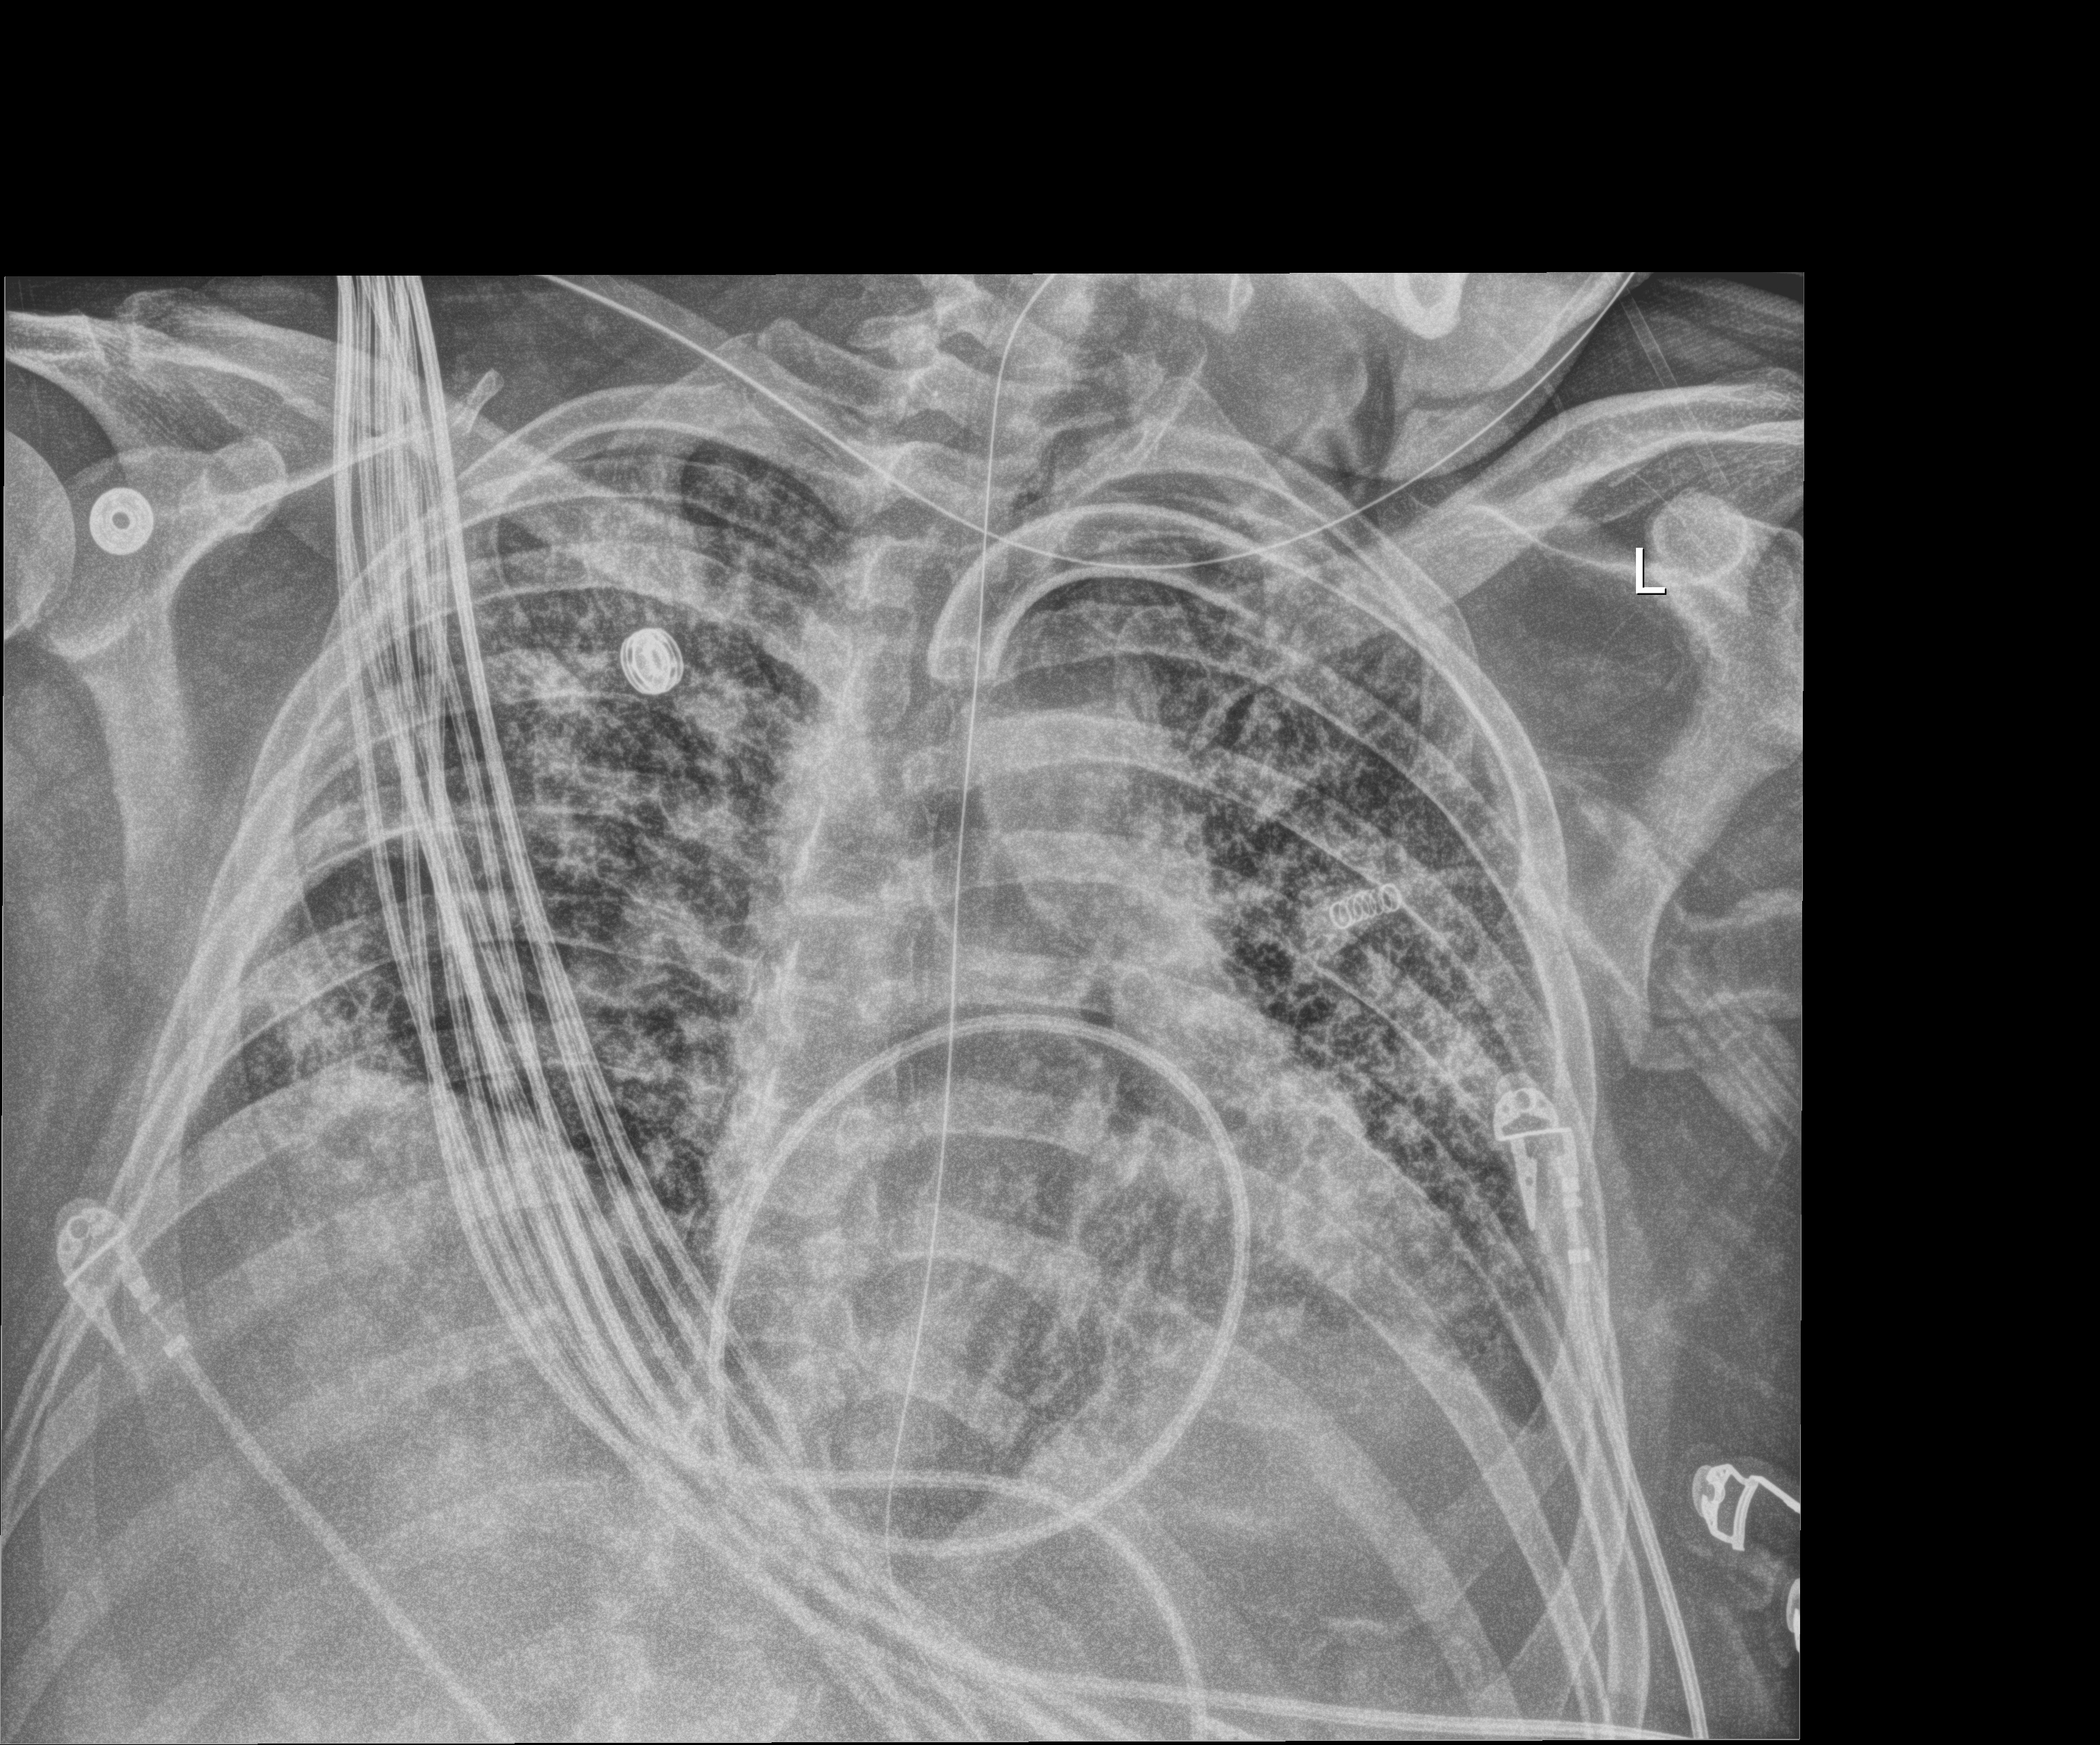
Chest X-ray (portable); anteroposterior (AP) projection. Male patient hospitalised with COVID-19, age 18–59 years.
Admission-level facts for this patient (not findings on this image; timing relative to this image not recorded): smoking status (admission record): never.